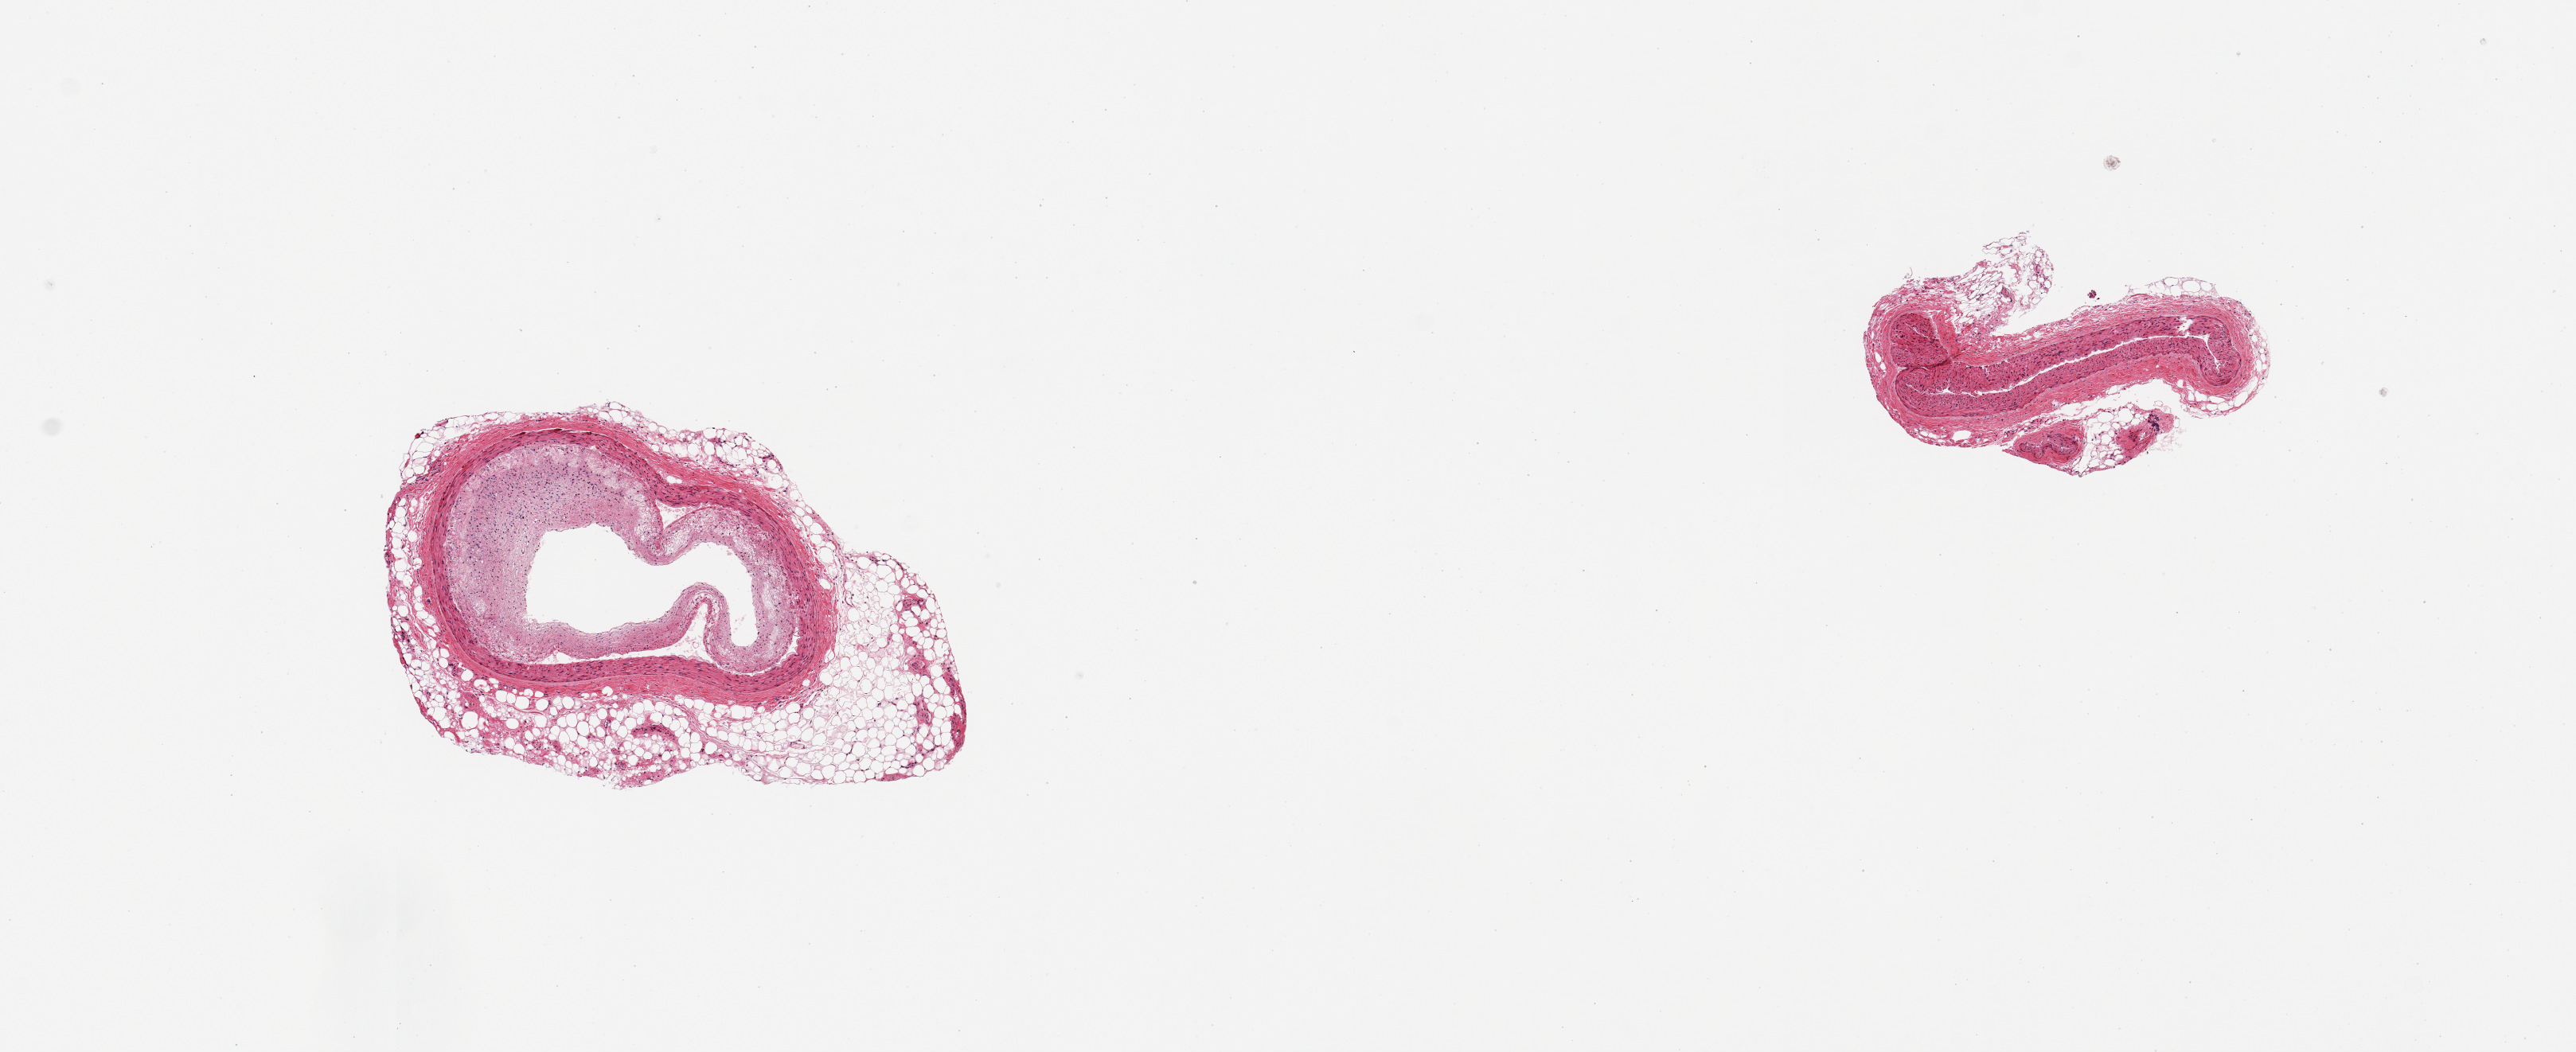
Whole-slide image, H&E stain — low-resolution overview of the scanned area, about 12.8 x 5.2 mm, PAXgene-fixed paraffin-embedded (PFPE) section, section of coronary artery (target tissue), tissue donor sample. Donor sex: female.
Reviewer comment on this tissue sample: 2 pieces, ~70% occlusive atherosis.